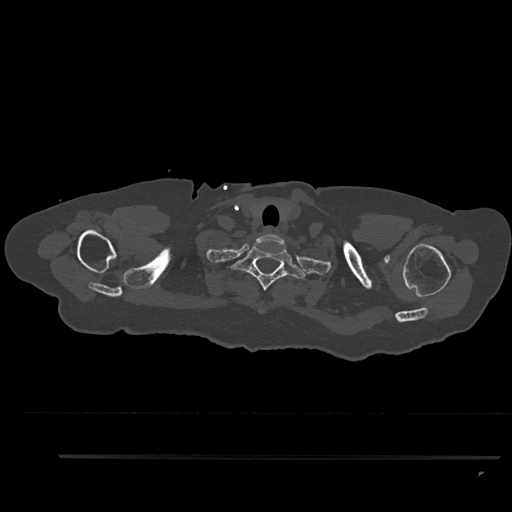
CT including the spine, one axial slice. Slice 766 of 797 in the series (ordered by position). Reconstruction kernel Br40s/3. Bone window (W 1800 / L 400 HU). 0.5 mm slice thickness. 512 × 512 image matrix. Patient: female, 44 years. From the clinical record (not read from this slice): primary cancer: renal; vertebrae with lytic lesions (as recorded): L1.
Structures marked on this image (semi-automatic segmentation, software-assisted and operator-edited):
- T1 vertebra: bounding box <231,246,306,291> (left, top, right, bottom; pixels)